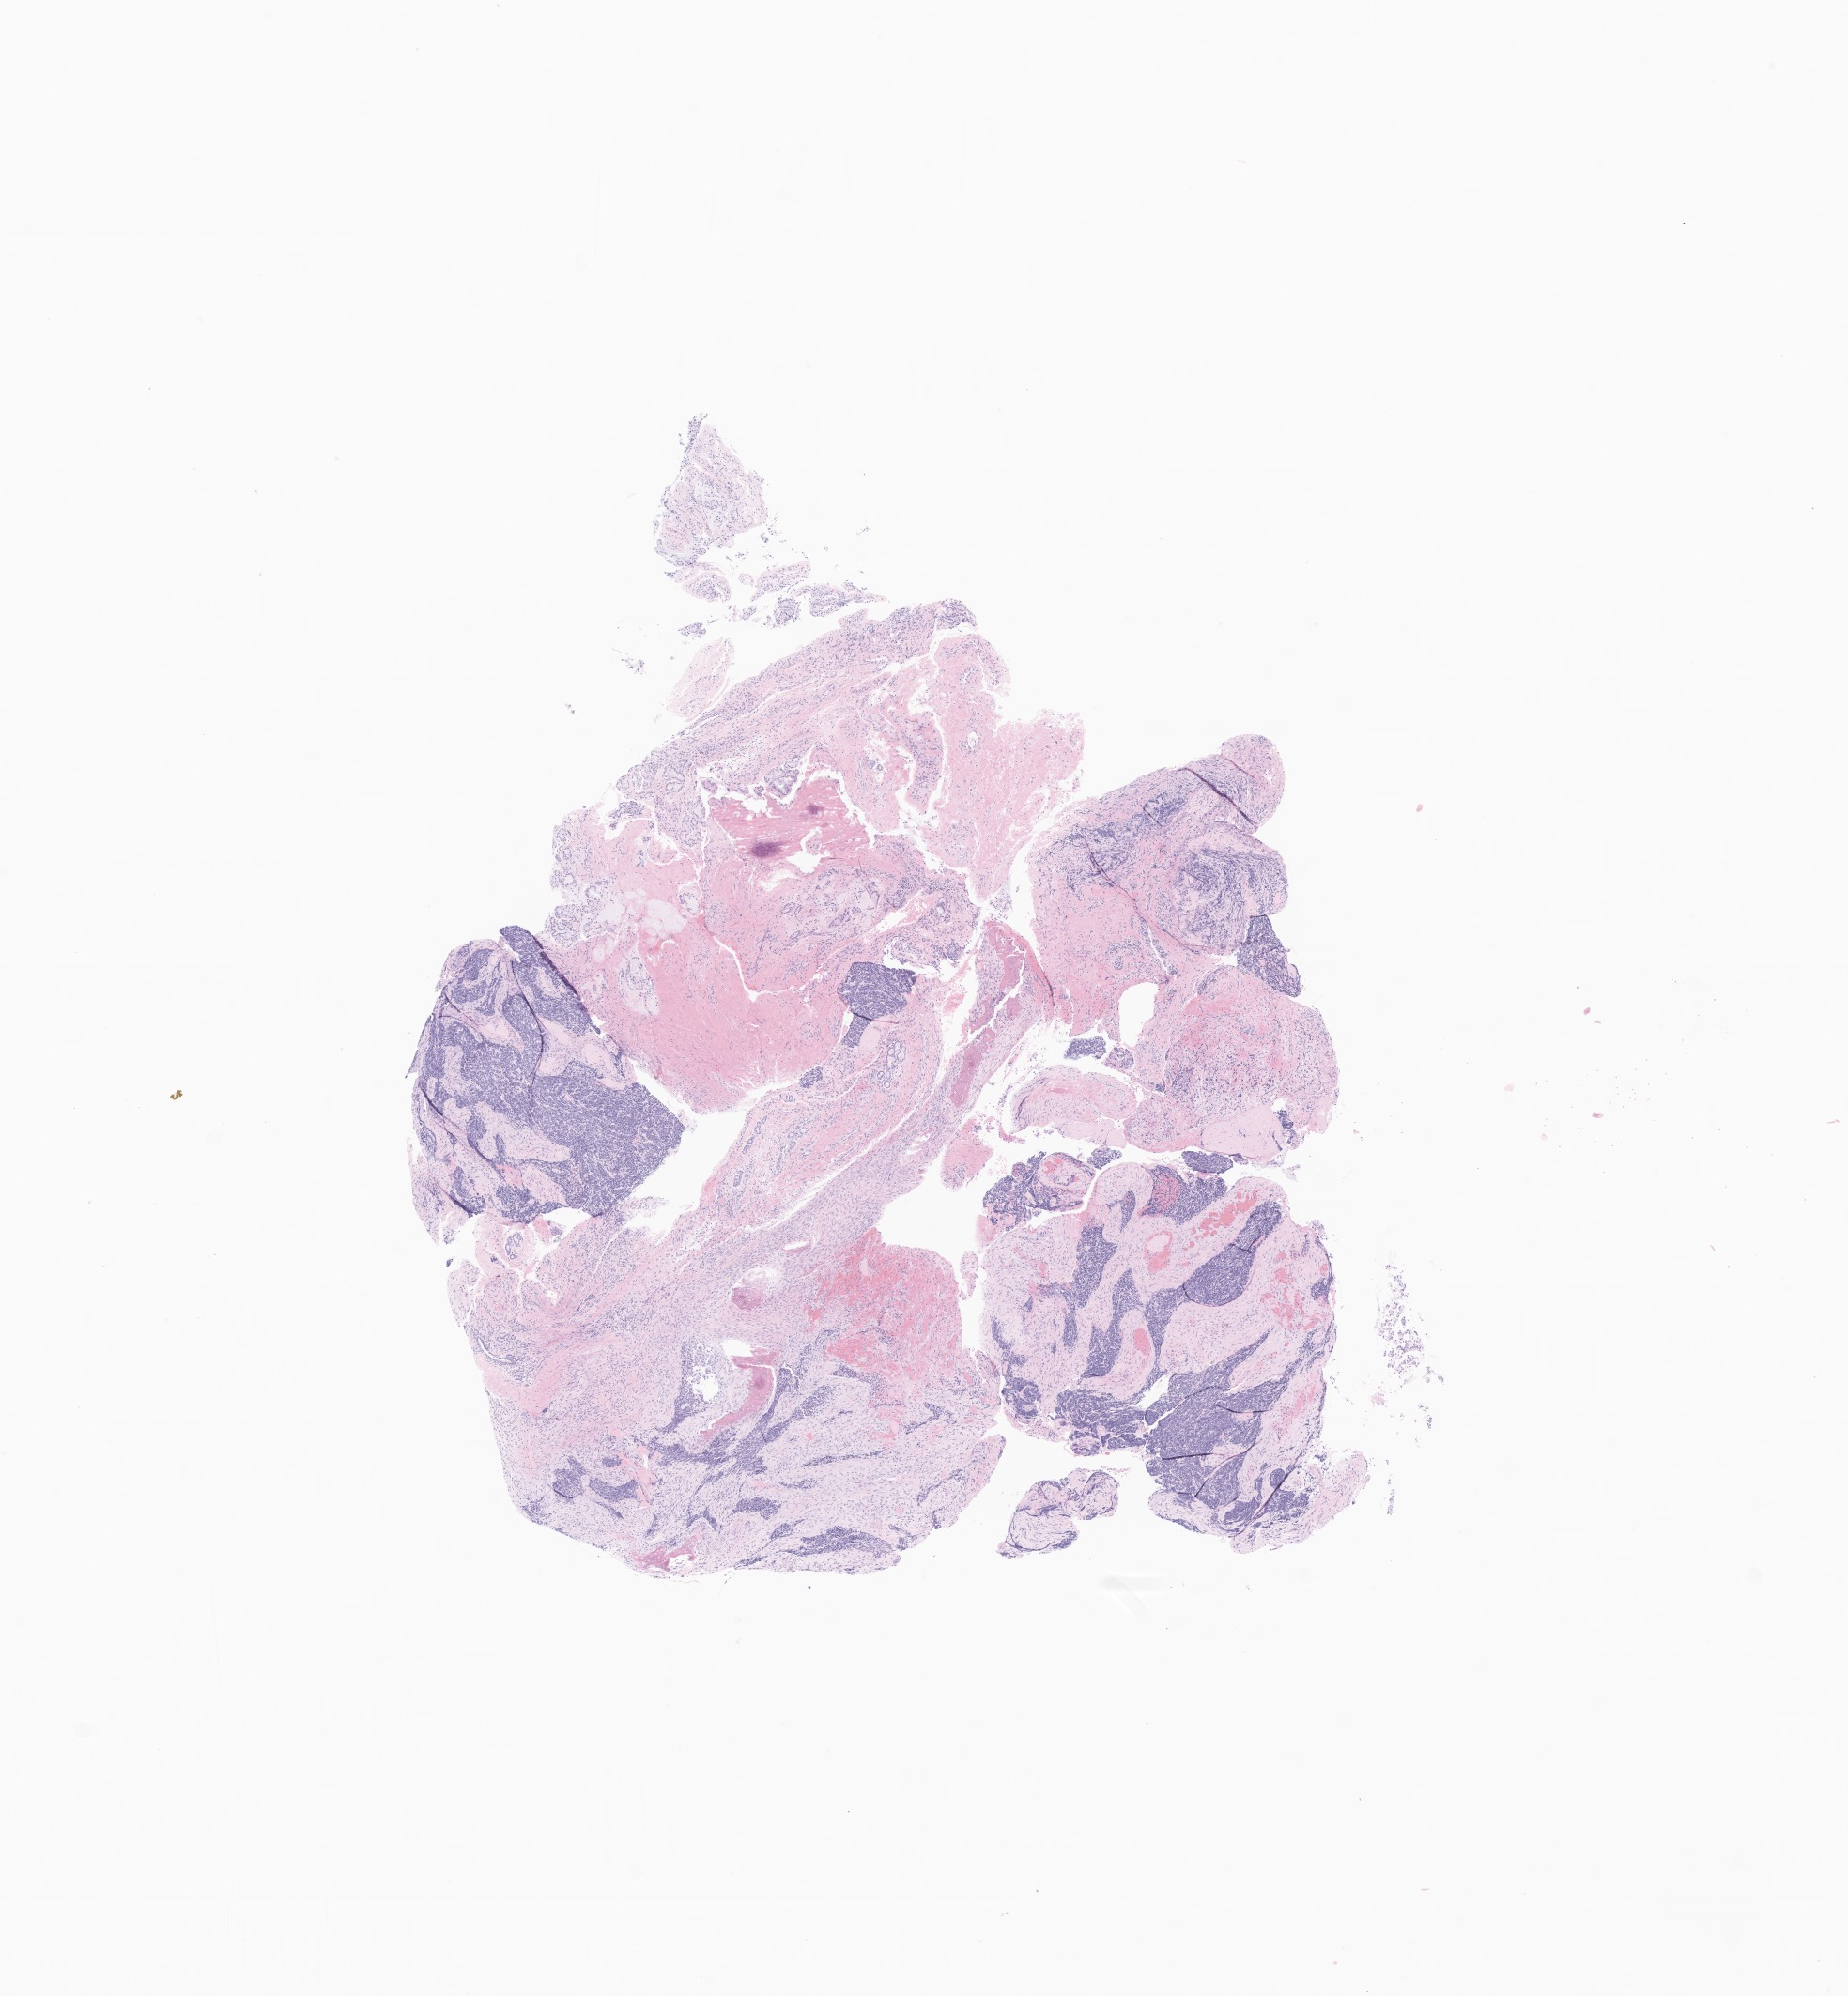
Haematoxylin and eosin whole-slide image of tumor tissue from the head and neck, low-resolution overview of the scanned area, about 8.3 x 9.0 mm, formalin-fixed paraffin-embedded section. Patient: female, age 47 months (3 years 11 months).
- diagnosis (ICD-O-3 morphology term): Neoplasm, uncertain whether benign or malignant